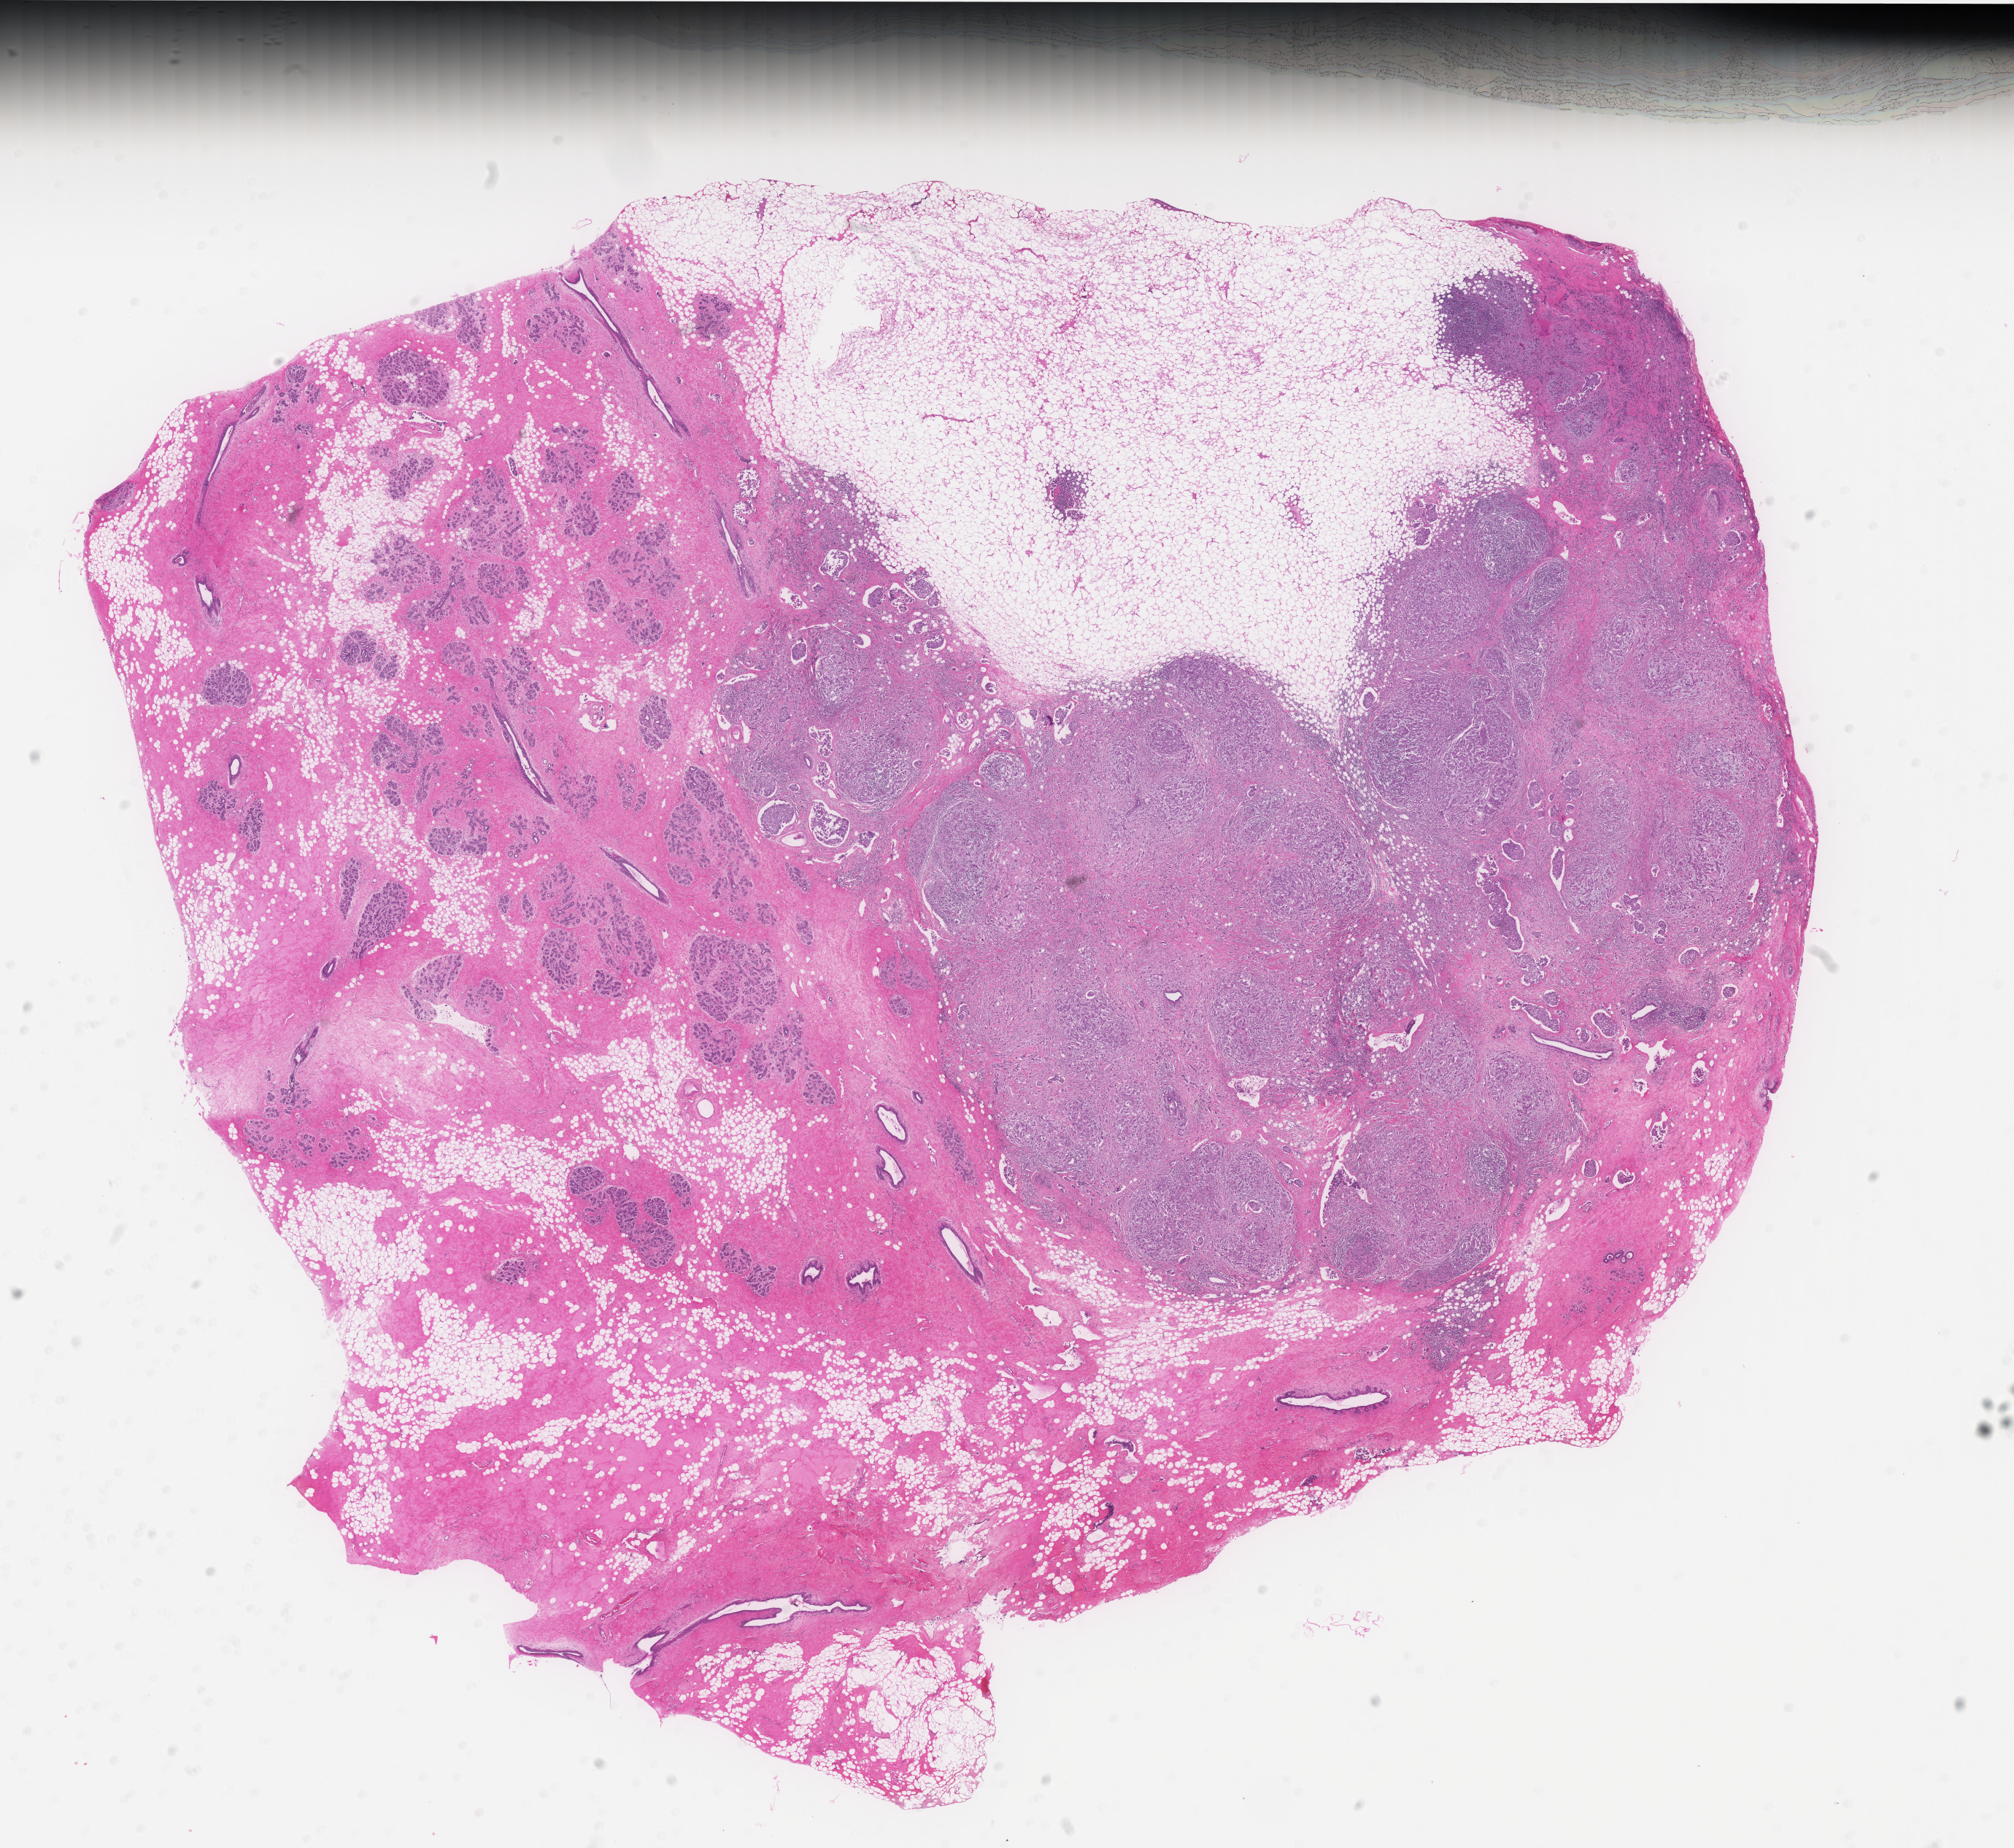
Whole-slide histology image, Hematoxylin and eosin (H&E) stained, low-resolution overview of the scanned area, about 22.1 x 20.3 mm (slide scanned at 40x). FFPE section. Breast, primary tumour sample. Patient: female, age at initial diagnosis 37 years.
* pathologic diagnosis: Infiltrating duct carcinoma, NOS
* laterality: right
* lymph nodes positive (case pathology): 9 of 14 examined
* AJCC pathologic stage: IIIA
* TNM: T3 N2a M0